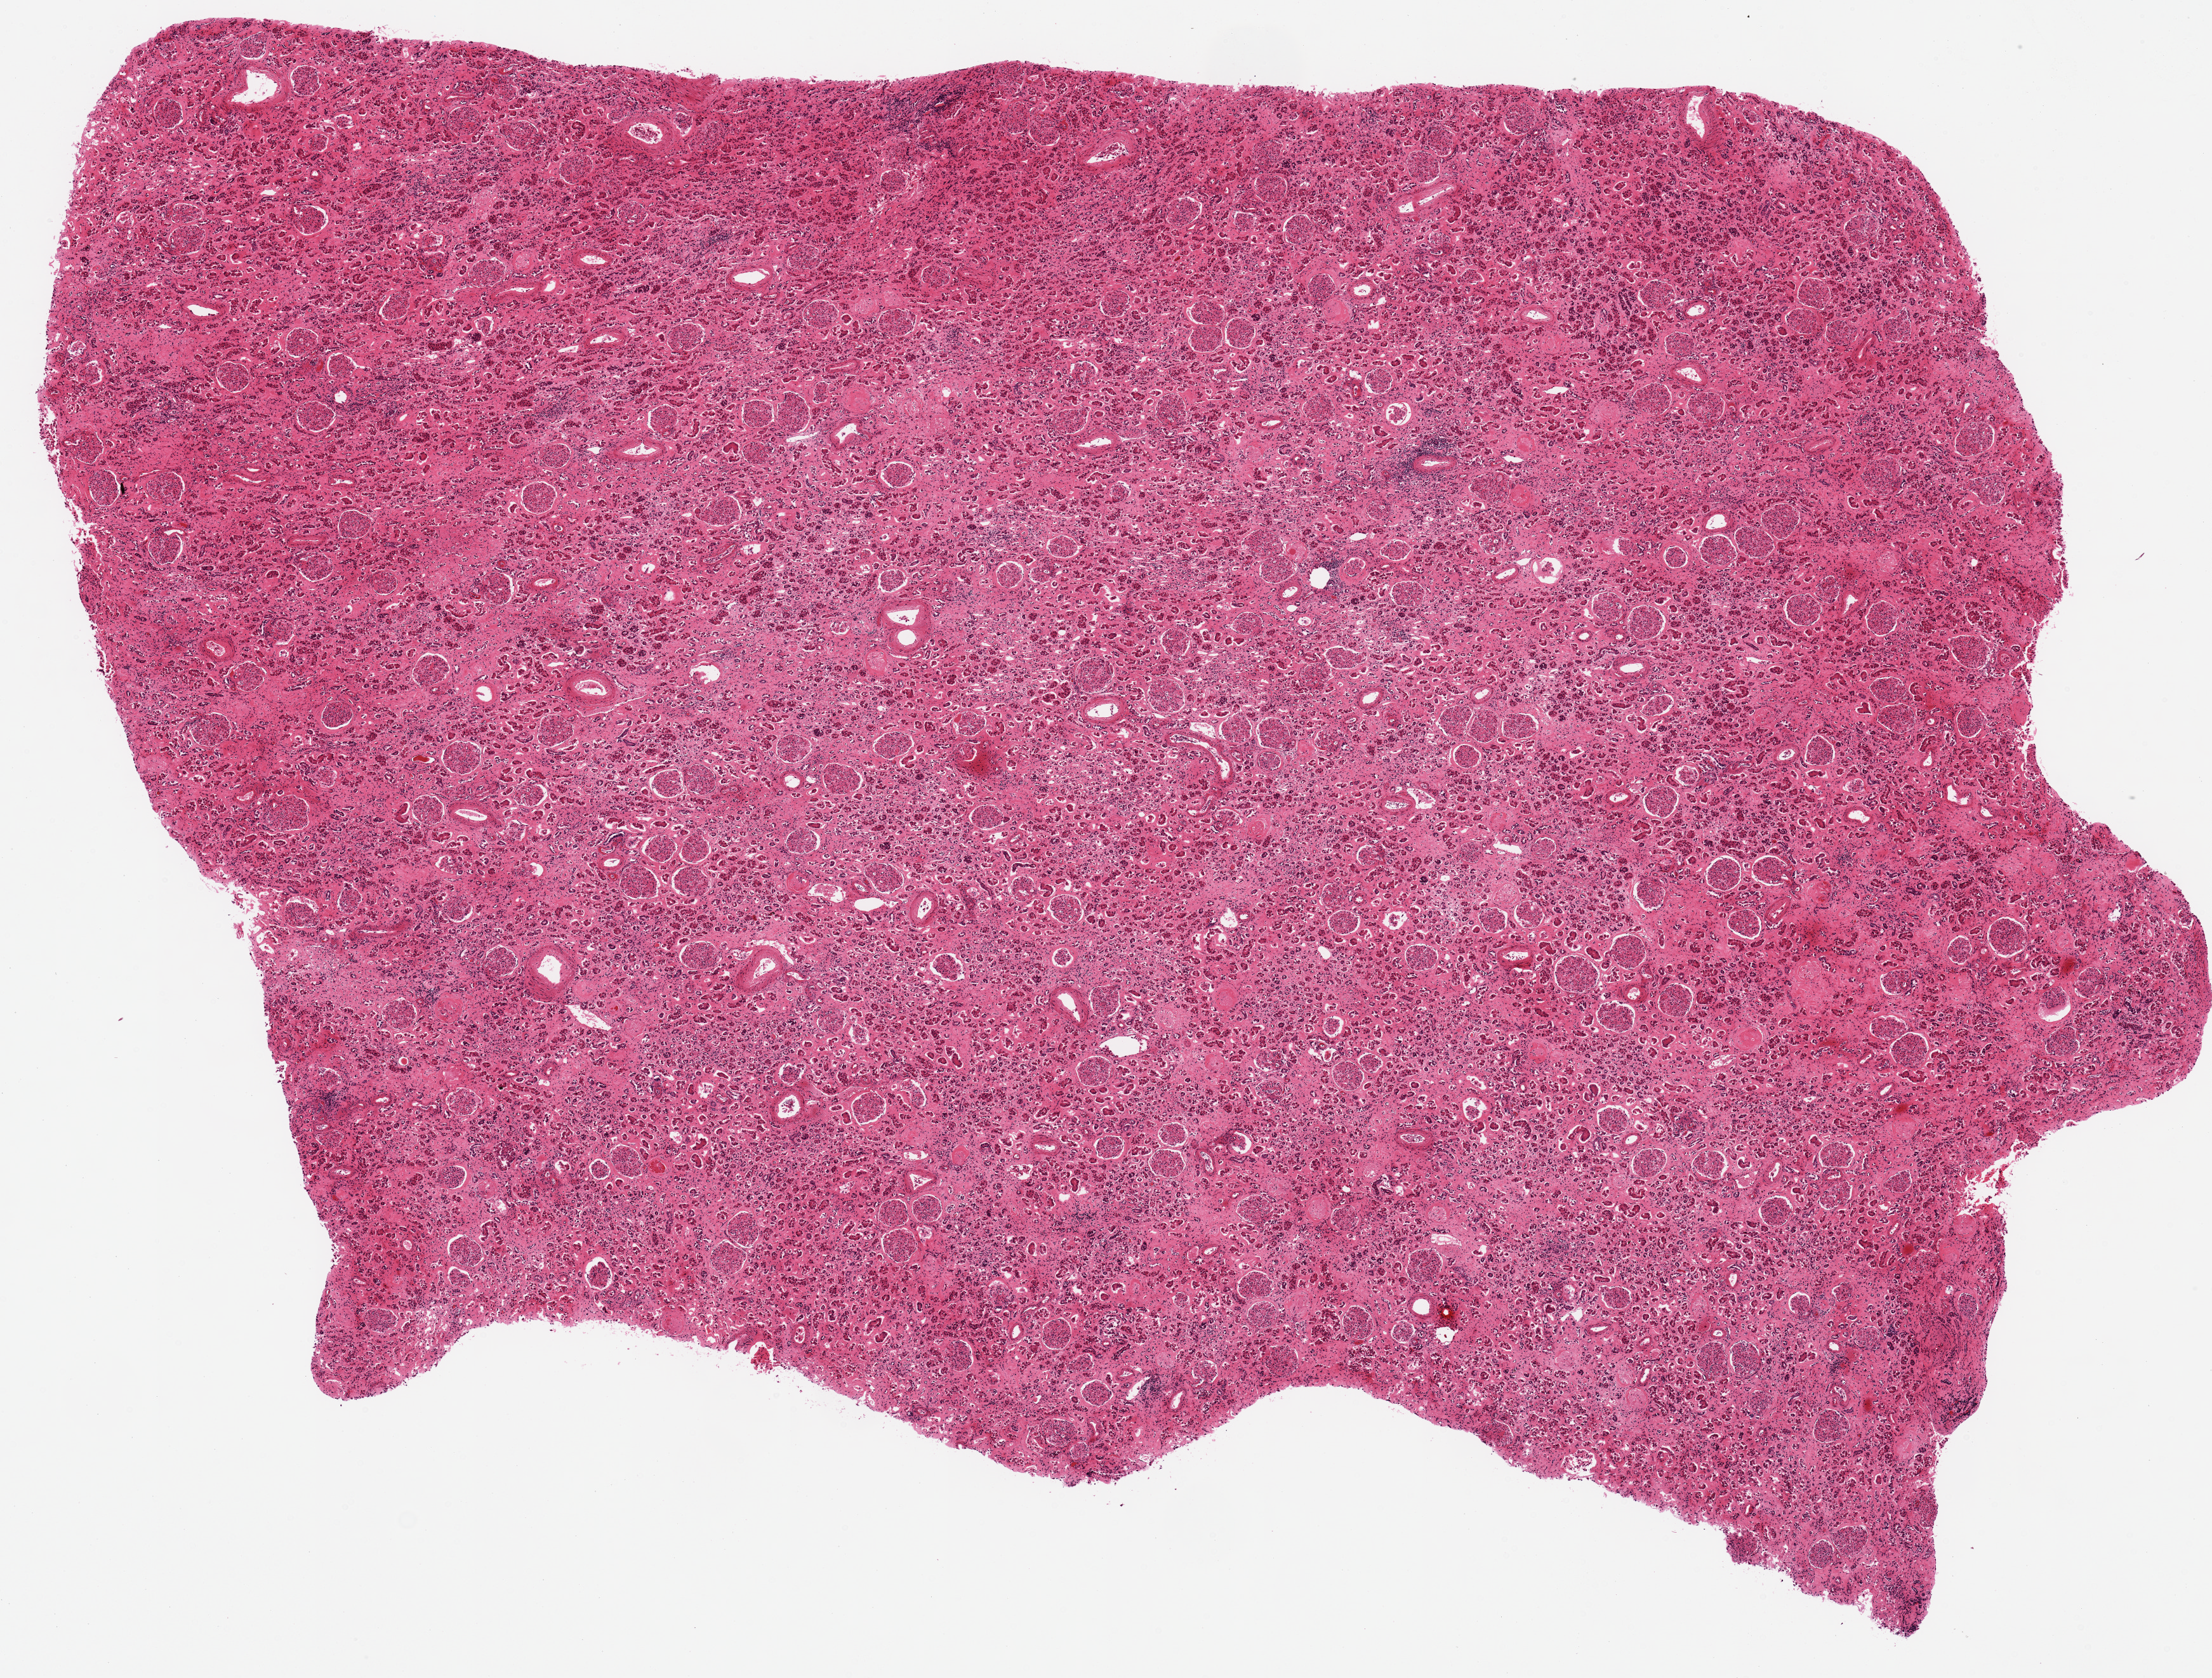
Hematoxylin and eosin (H&E) whole-slide image, whole scanned area (about 13.8 x 10.5 mm) shown as a low-resolution overview; PAXgene-fixed paraffin-embedded (PFPE) section; sampled site (target tissue): renal cortex; tissue donor sample. Donor sex: male.
Reviewer comment on this tissue sample: cortex, not medulla.